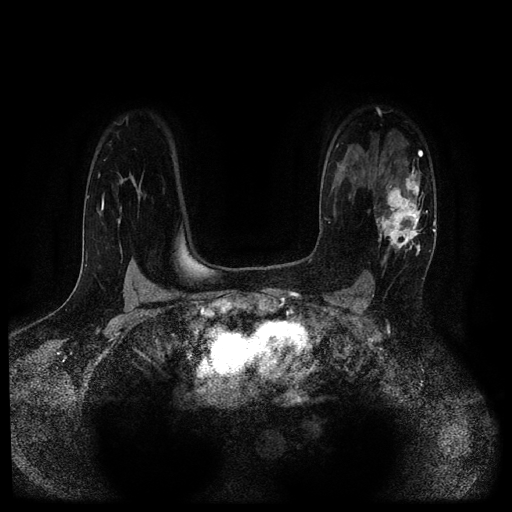
Breast MRI (dynamic contrast-enhanced, multi-phase), one axial slice; position 75 of 116 along the scan axis; dynamic contrast-enhanced series, time point 2 of 5 at this slice position (early post-contrast); 1.5 T; TE 2.7 ms, TR 5.4 ms; 512 × 512 image matrix. Female patient, age 43 years.
Annotated regions visible in this slice (semi-automatically segmented with operator editing):
- breast lesion (labelled 'tumour' in the annotation; benign lesions carry a separate 'benign' label): bounding box (x1, y1, x2, y2) in pixels: (376, 159, 429, 267)